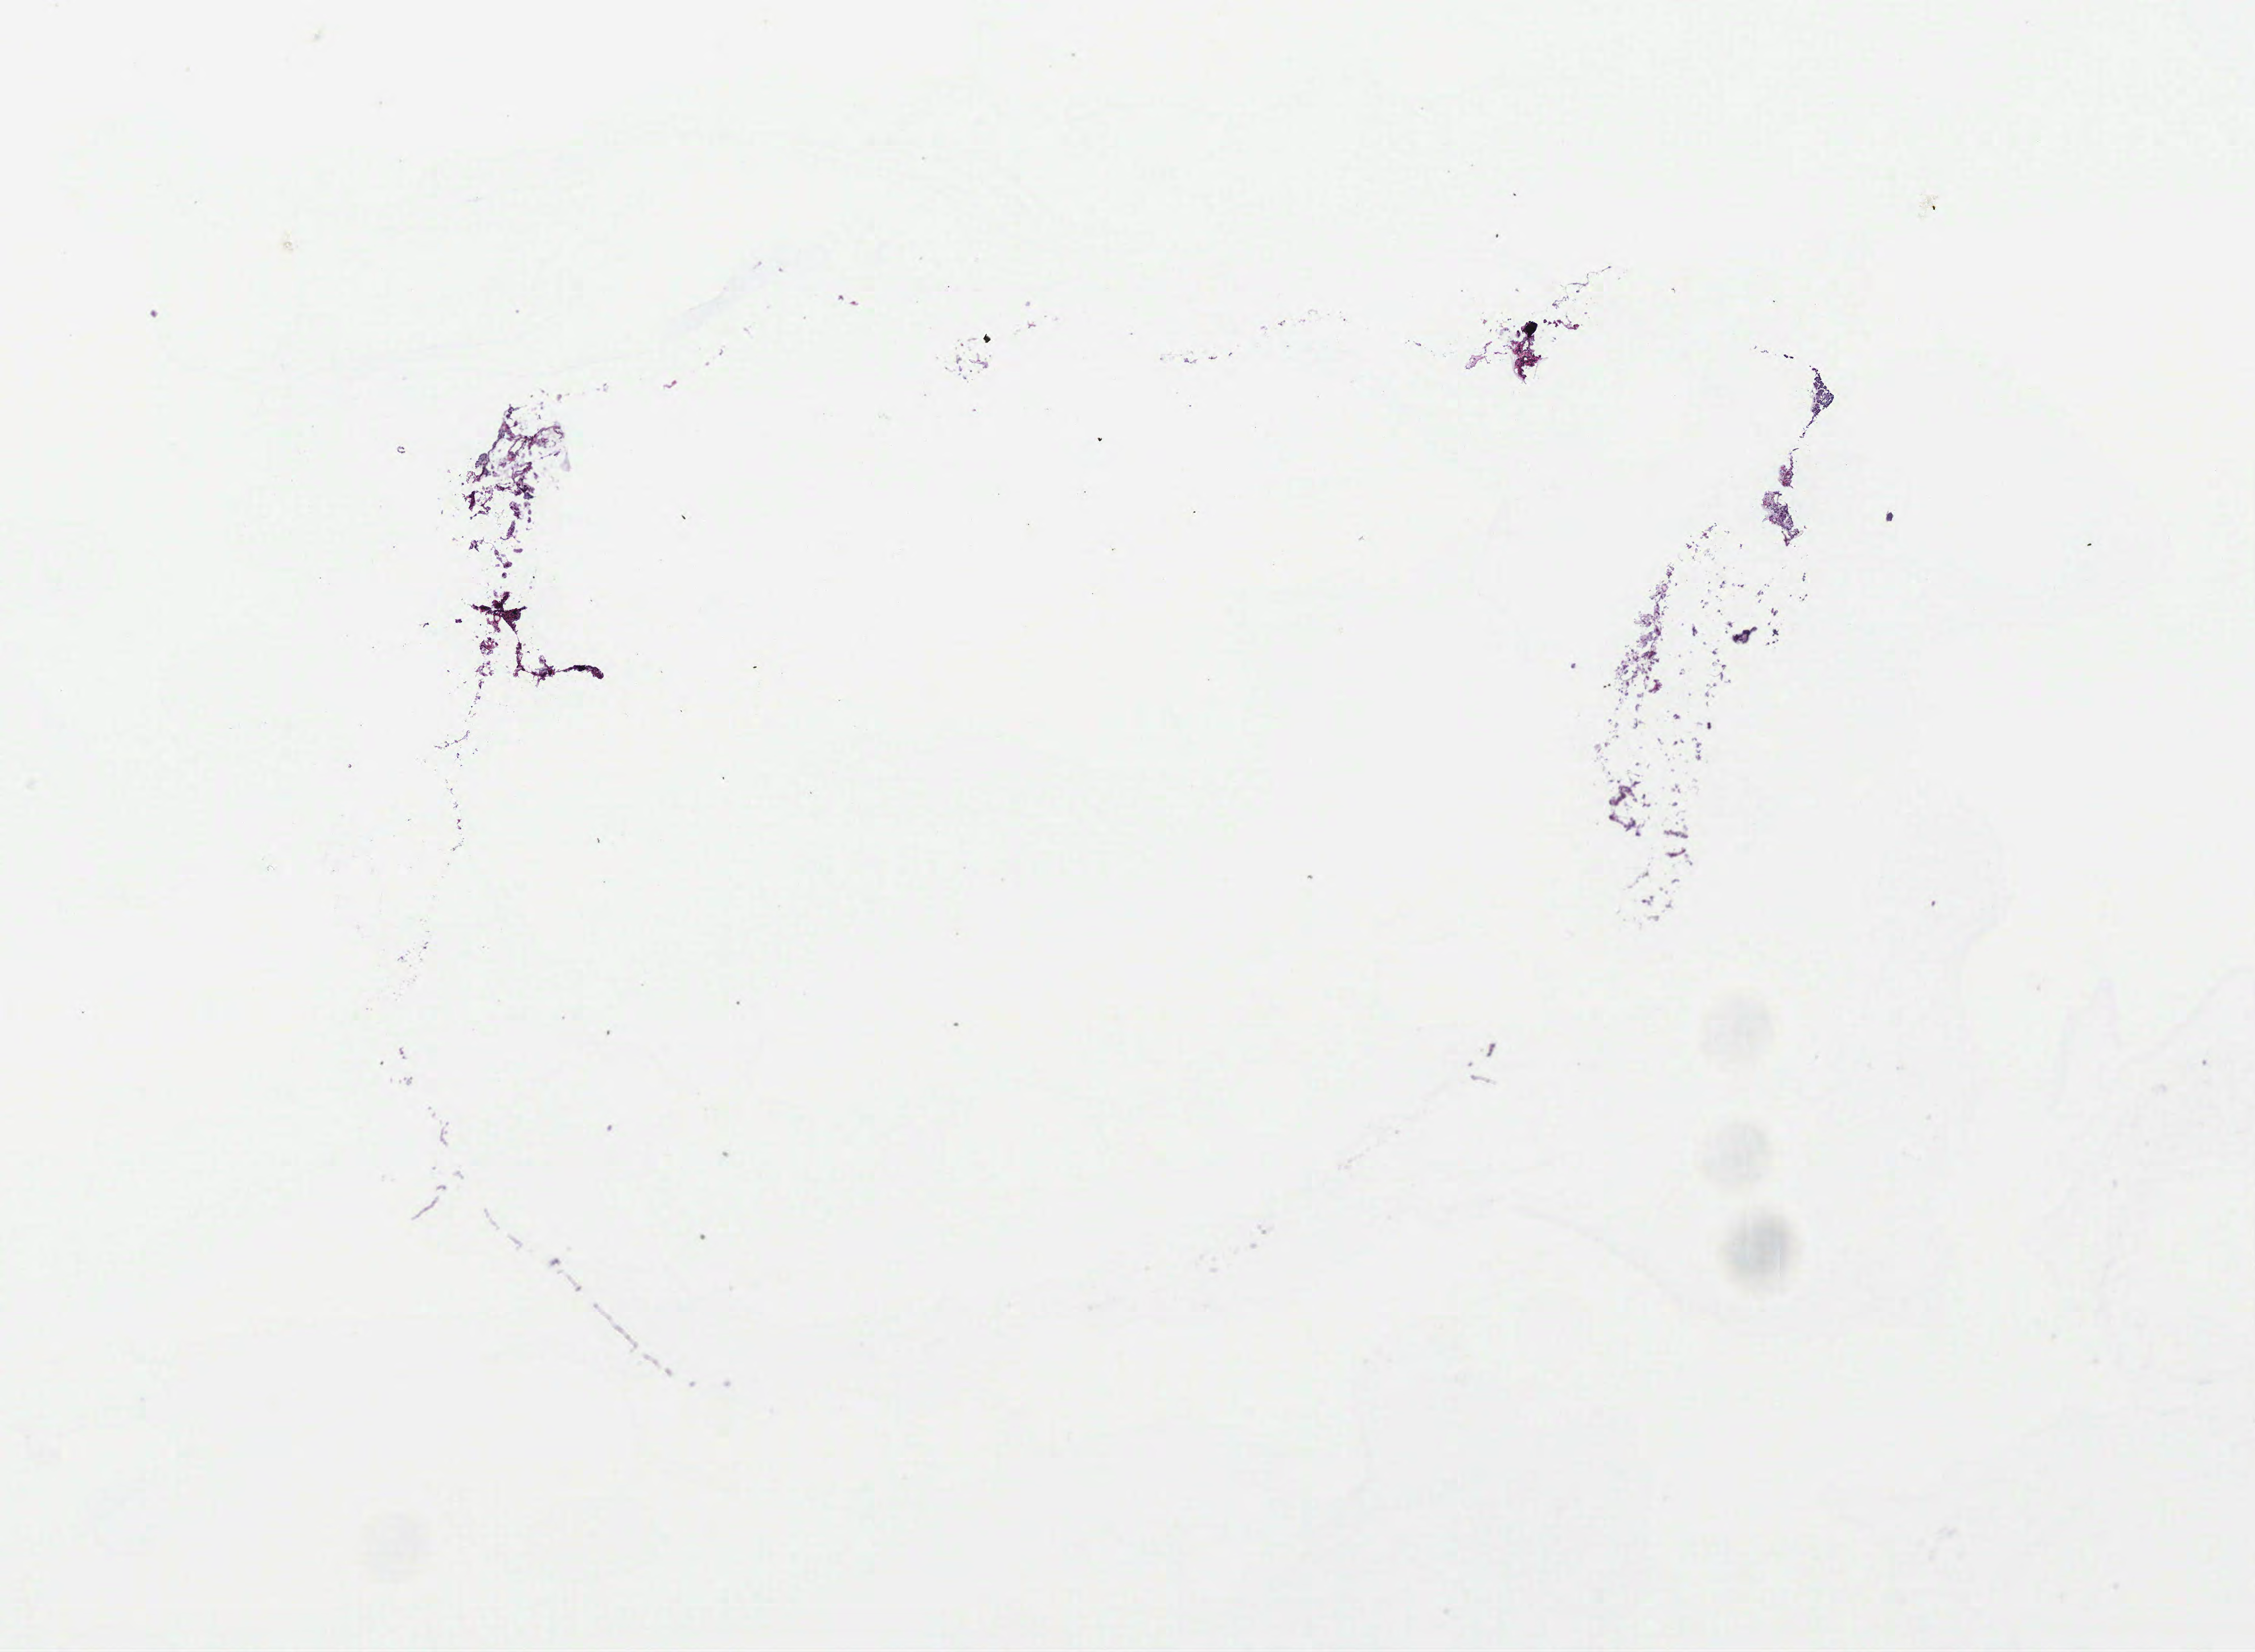
Digitized Hematoxylin and eosin (H&E) stained tissue section (whole slide) — whole scanned area (about 15.8 x 11.6 mm) shown as a low-resolution overview; ovary, tissue type not recorded.
* patient diagnosis (cohort enrolment): ovarian cancer (ovary)